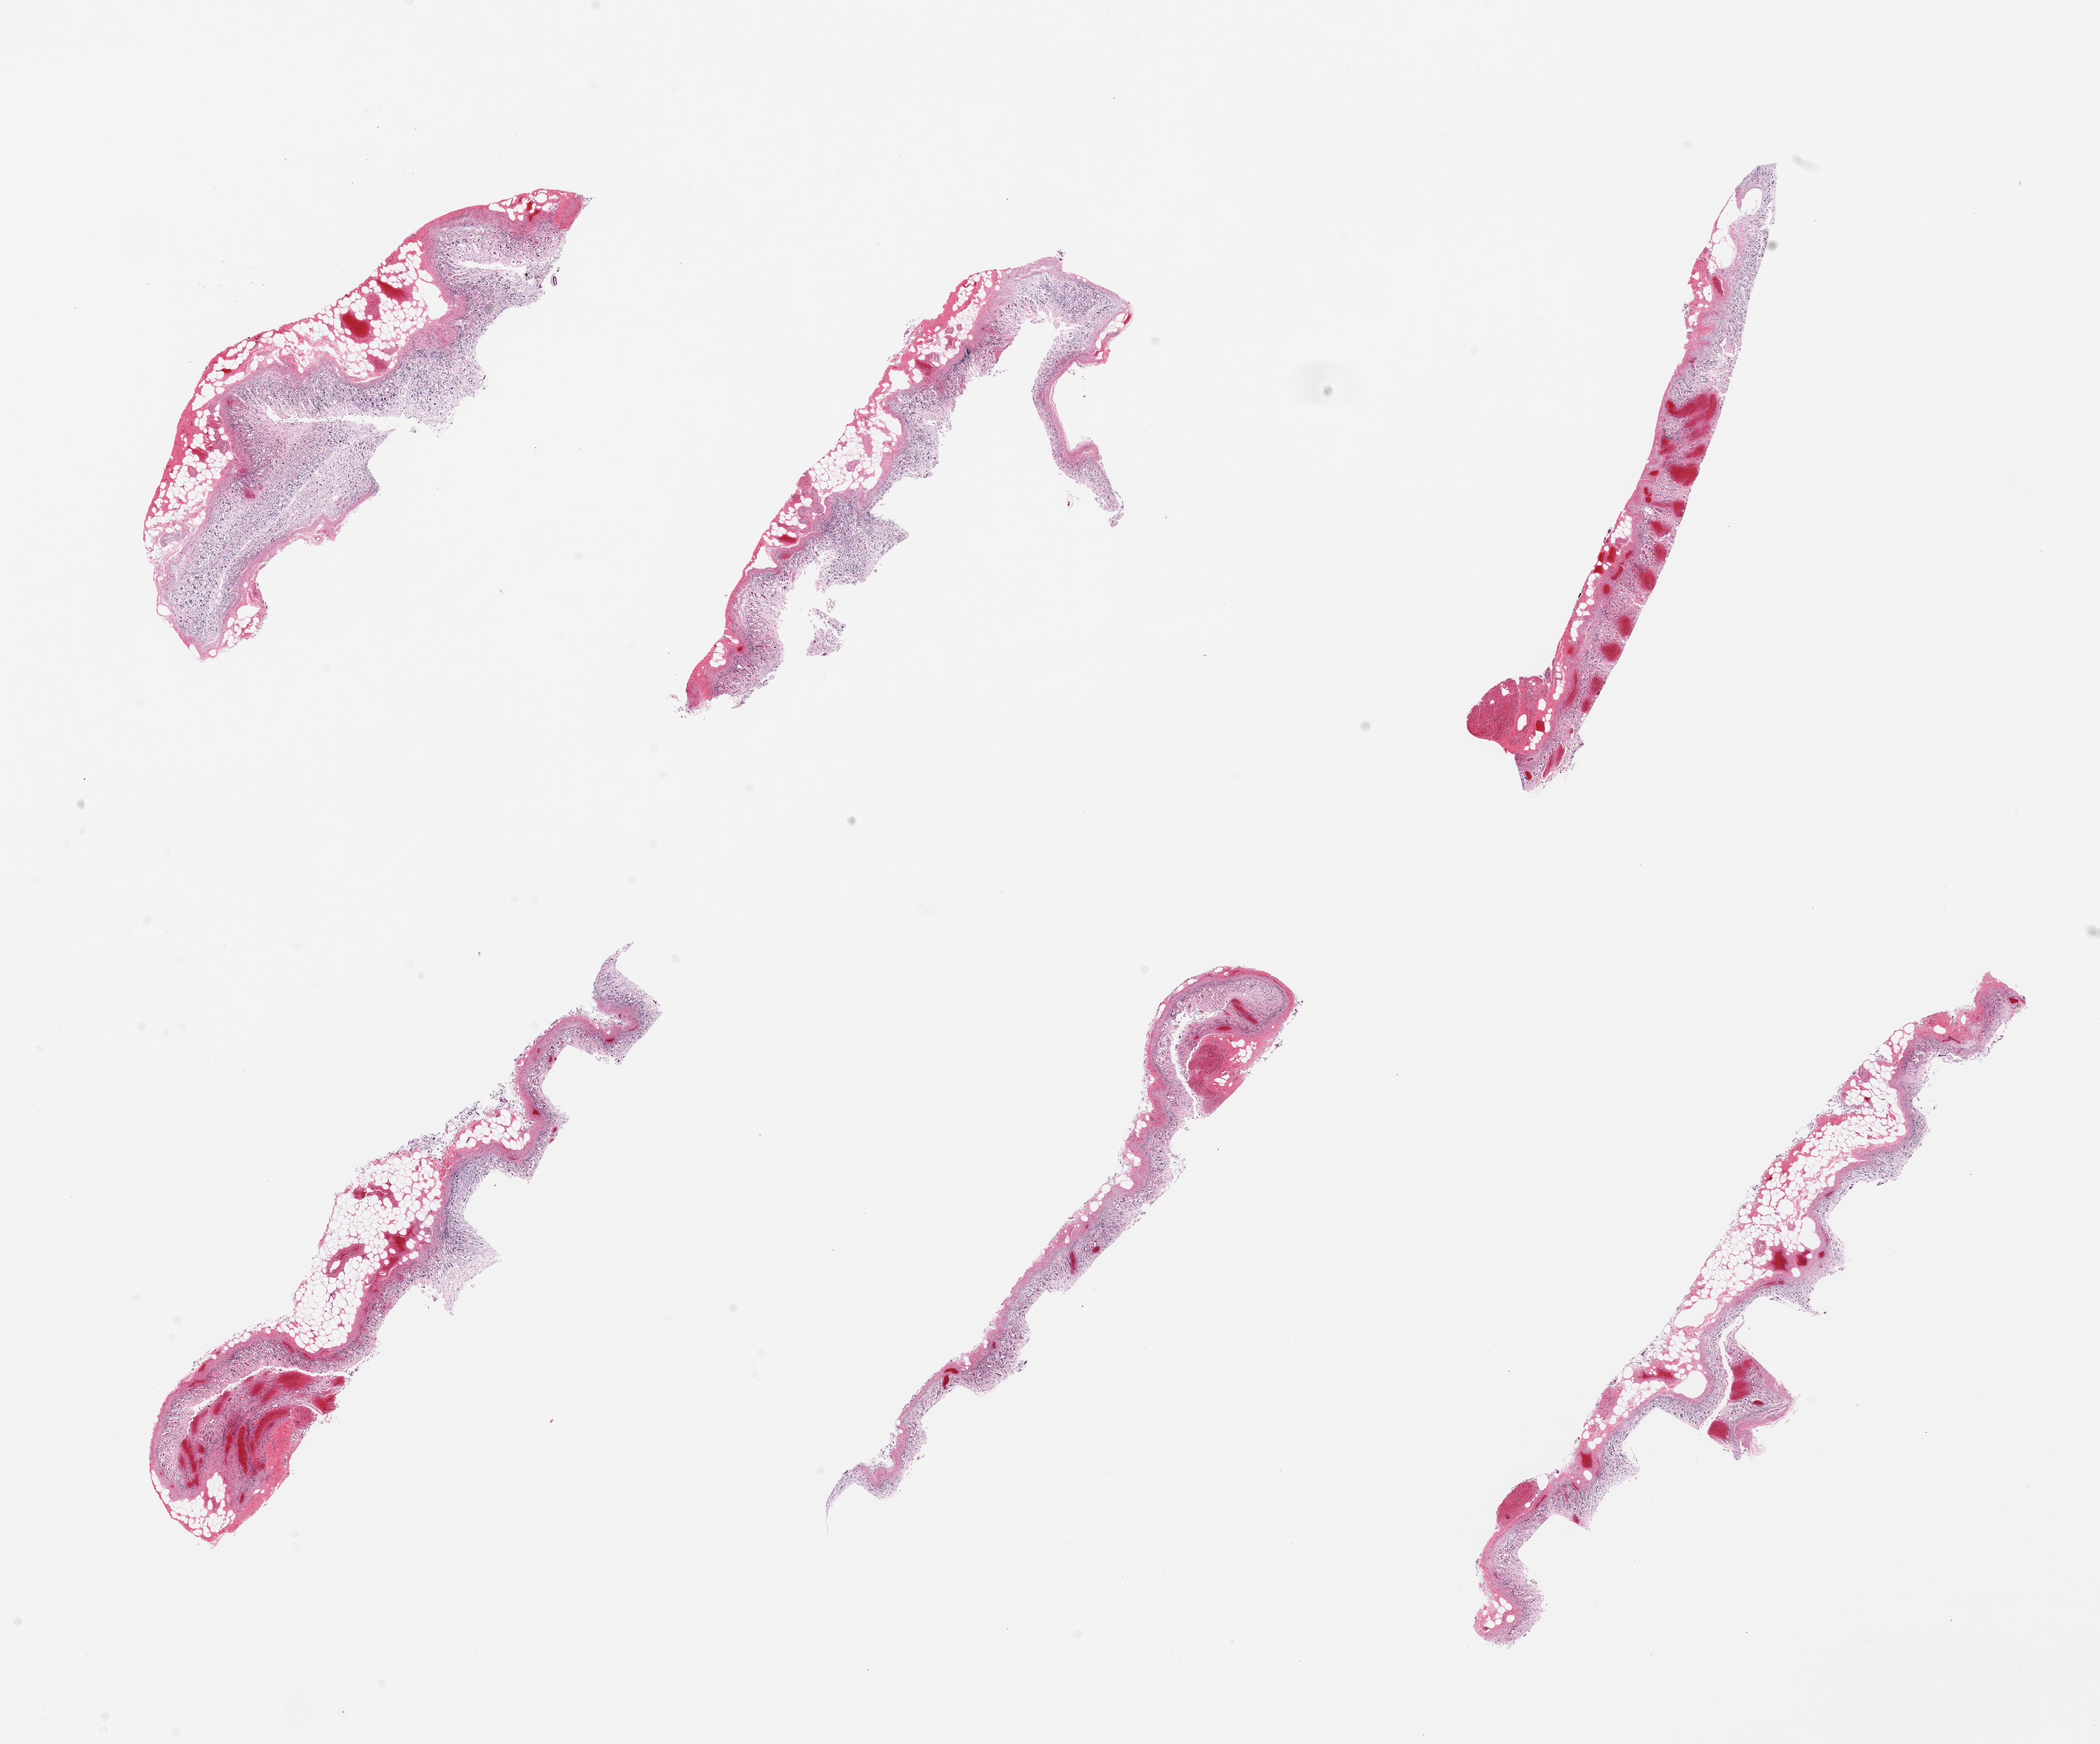
Digitized hematoxylin and eosin (H&E)-stained section, a low-resolution overview of the entire scanned area, about 24.6 x 20.4 mm (acquisition: 20x scan); PAXgene-fixed, paraffin-embedded tissue; target tissue: stomach; donor tissue sample. Donor sex: male.
- reviewer comment on this tissue sample: 6 pieces, severely autolyzed mucosa